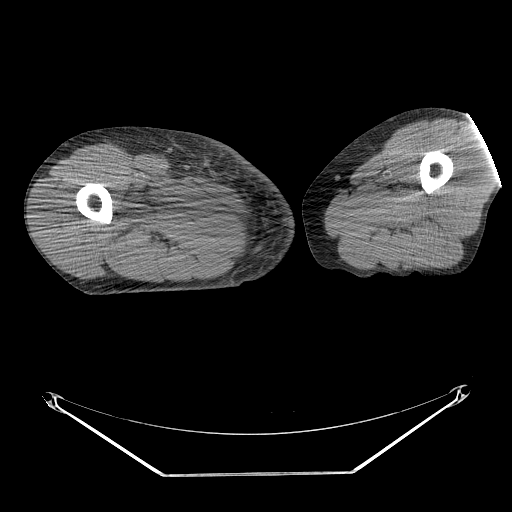
CT of an extremity soft-tissue mass (from a PET/CT study), one axial slice. Slice 239 of 311 in the series (ordered by position). 140 kVp. Soft-tissue window (W 400 / L 40 HU). 3.75 mm slice thickness. 512 × 512 image matrix, field of view 500 × 500 mm. Male patient. From the clinical record (not read from this slice): histological type: undifferentiated - pleiomorphic; grade: high; site of the primary tumour: right thigh.
Outlined on this slice (expert contour drawn on MRI and transferred to this co-registered scan by the dataset authors):
- gross tumour volume including surrounding oedema: bounding box <130,178,209,232> (left, top, right, bottom; pixels)